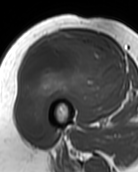
MRI of an extremity soft-tissue mass, one axial slice. Slice 53 of 99 in the series (ordered by position). MR volume resampled by the dataset authors to the PET/CT grid (not the native acquisition matrix). 3.27 mm slice thickness. 138 × 172 image matrix. Female patient. Case-level facts recorded for this patient, not image findings: histological type: pleiomorphic undifferentiated sarcoma; grade: high; site of the primary tumour: right quadricep.
Annotated regions visible in this slice (expert contour drawn on MRI and transferred to this co-registered scan by the dataset authors):
- gross tumour volume including surrounding oedema: bounding box (x1, y1, x2, y2) in pixels: (16, 32, 125, 138)
- gross tumour volume (mass): (16, 32, 125, 138)